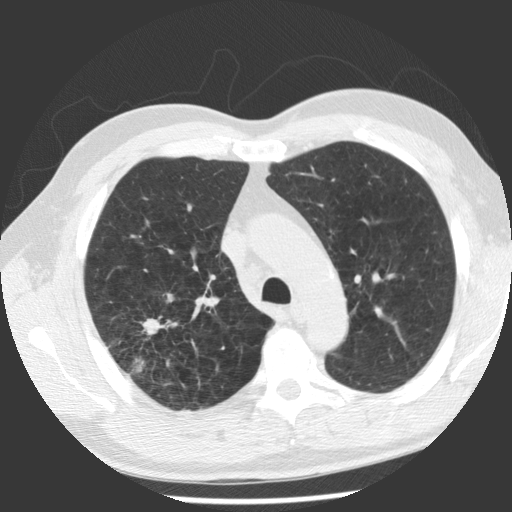
Axial slice from a low-dose chest CT screening exam, baseline annual screen, lung window (W 1500 / L -600 HU), 140 kVp, 512 × 512 image matrix, field of view 344 × 344 mm. Male participant, aged 62 years at enrolment. Former smoker at enrolment.
- Lesion marked by an expert reader, box from (x=112, y=300) to (x=188, y=375) px.
- The screening reader recorded 2 non-calcified nodules or masses ≥4 mm on this exam; which of them this box marks is not recorded.
- Later outcome: lung cancer diagnosed 71 days after this screen — adenocarcinoma, NOS, right upper lobe, poorly differentiated (G3), stage IV (AJCC 6th edition), 30 mm at pathology.